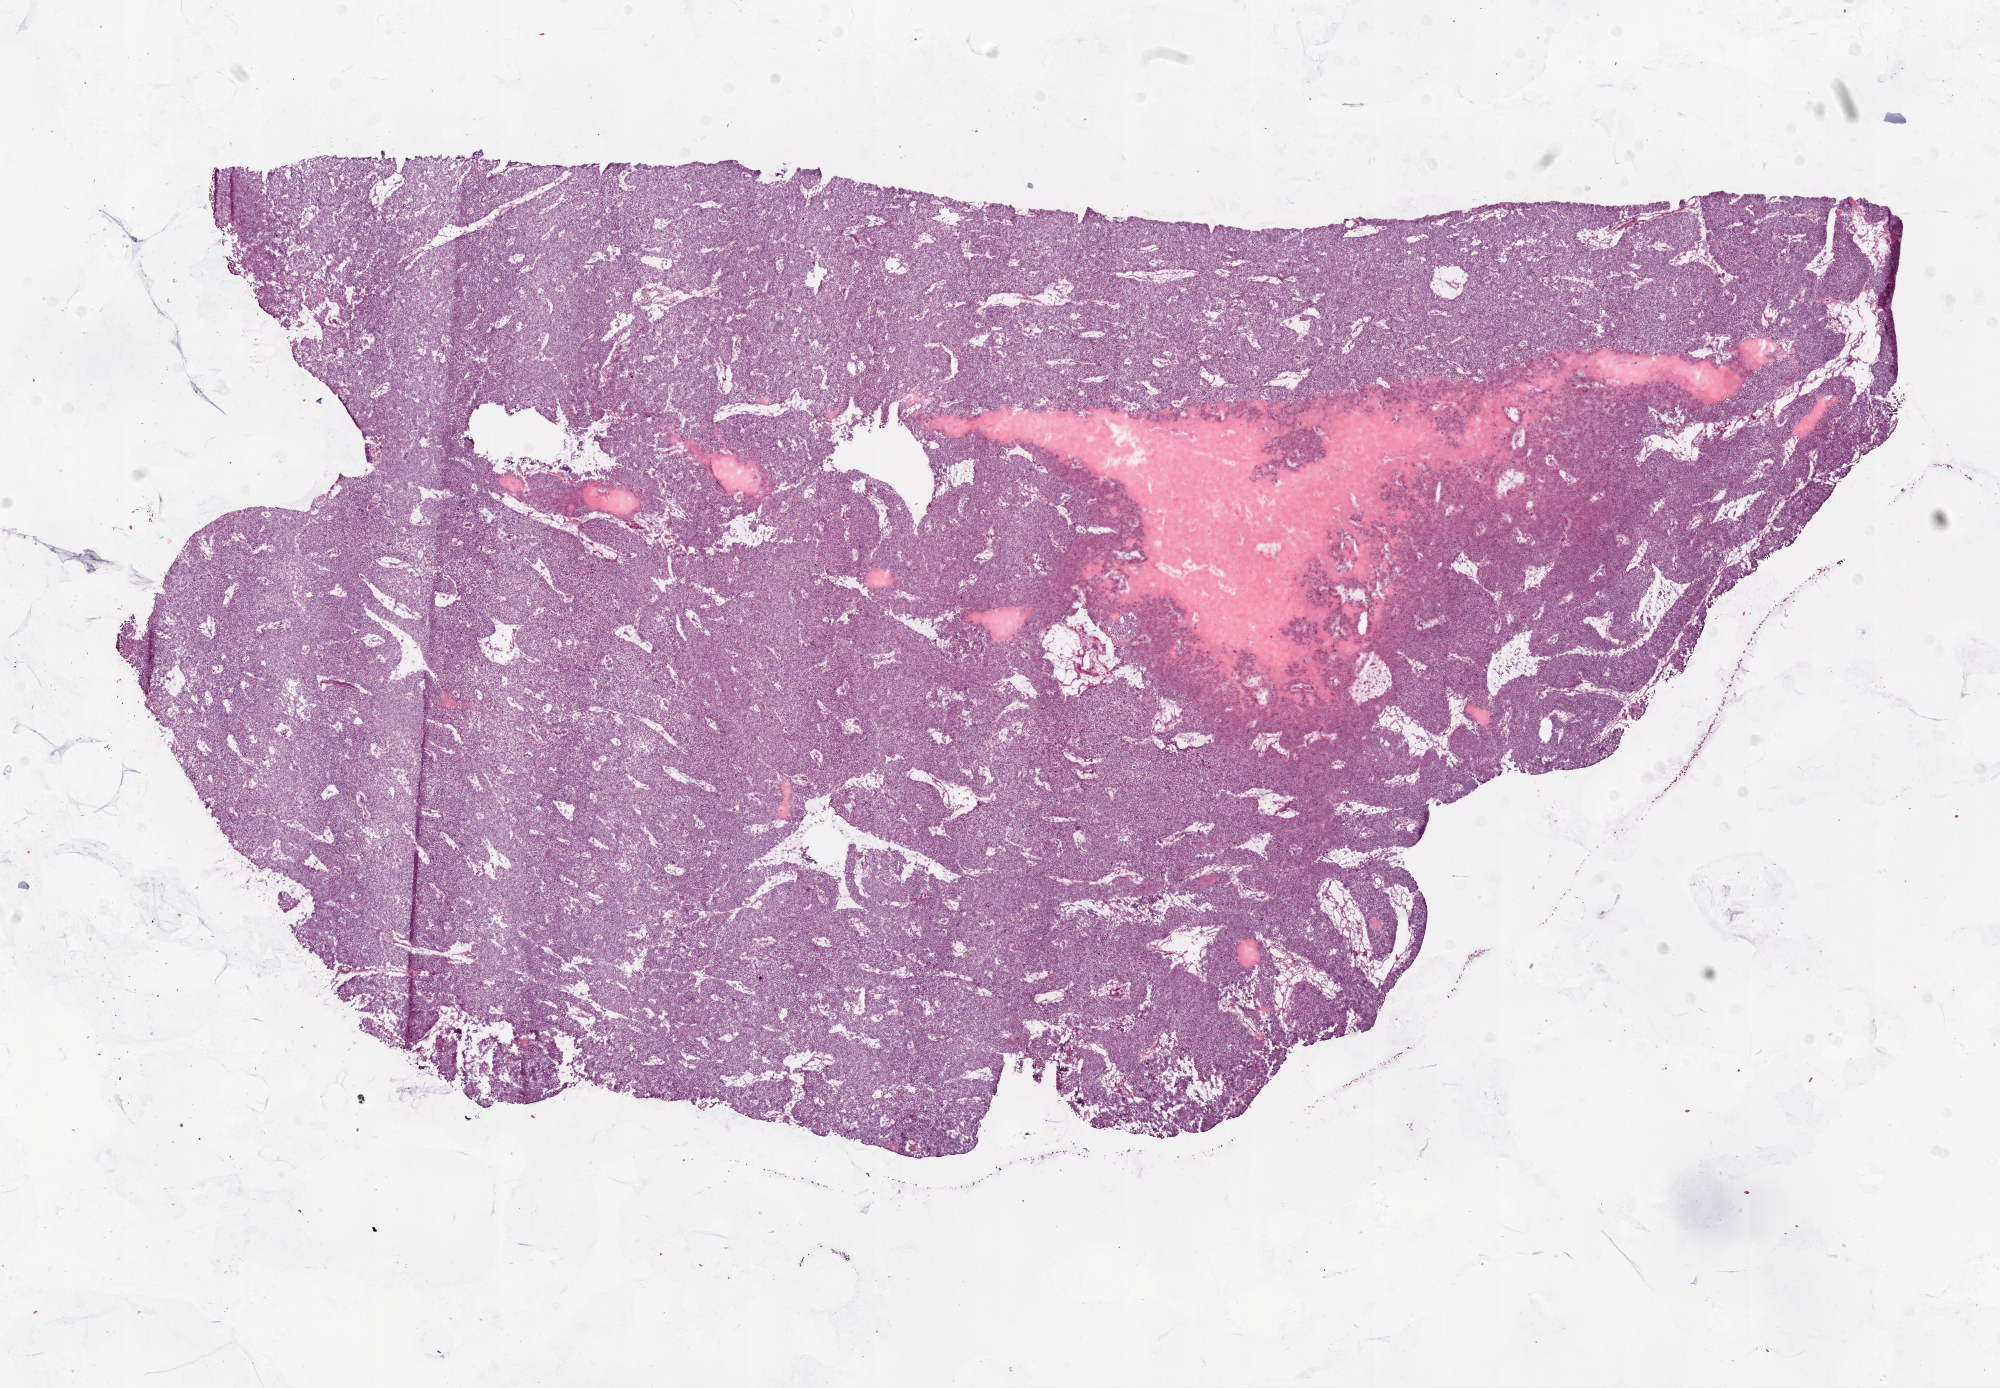
H&E whole-slide image, low-resolution overview of the scanned area, about 16.0 x 11.1 mm (slide scanned at 20x); frozen section; primary tumour sample from the ovary. Female, age 49 years at initial diagnosis. Histologic grade: G3 (poorly differentiated). Pathologist review of this section (percent, as recorded): tumour cells 94%, tumour nuclei 95%, normal cells 0%, stromal cells 5%, necrosis 1%.
• diagnosis: Serous cystadenocarcinoma, NOS
• FIGO stage: IC